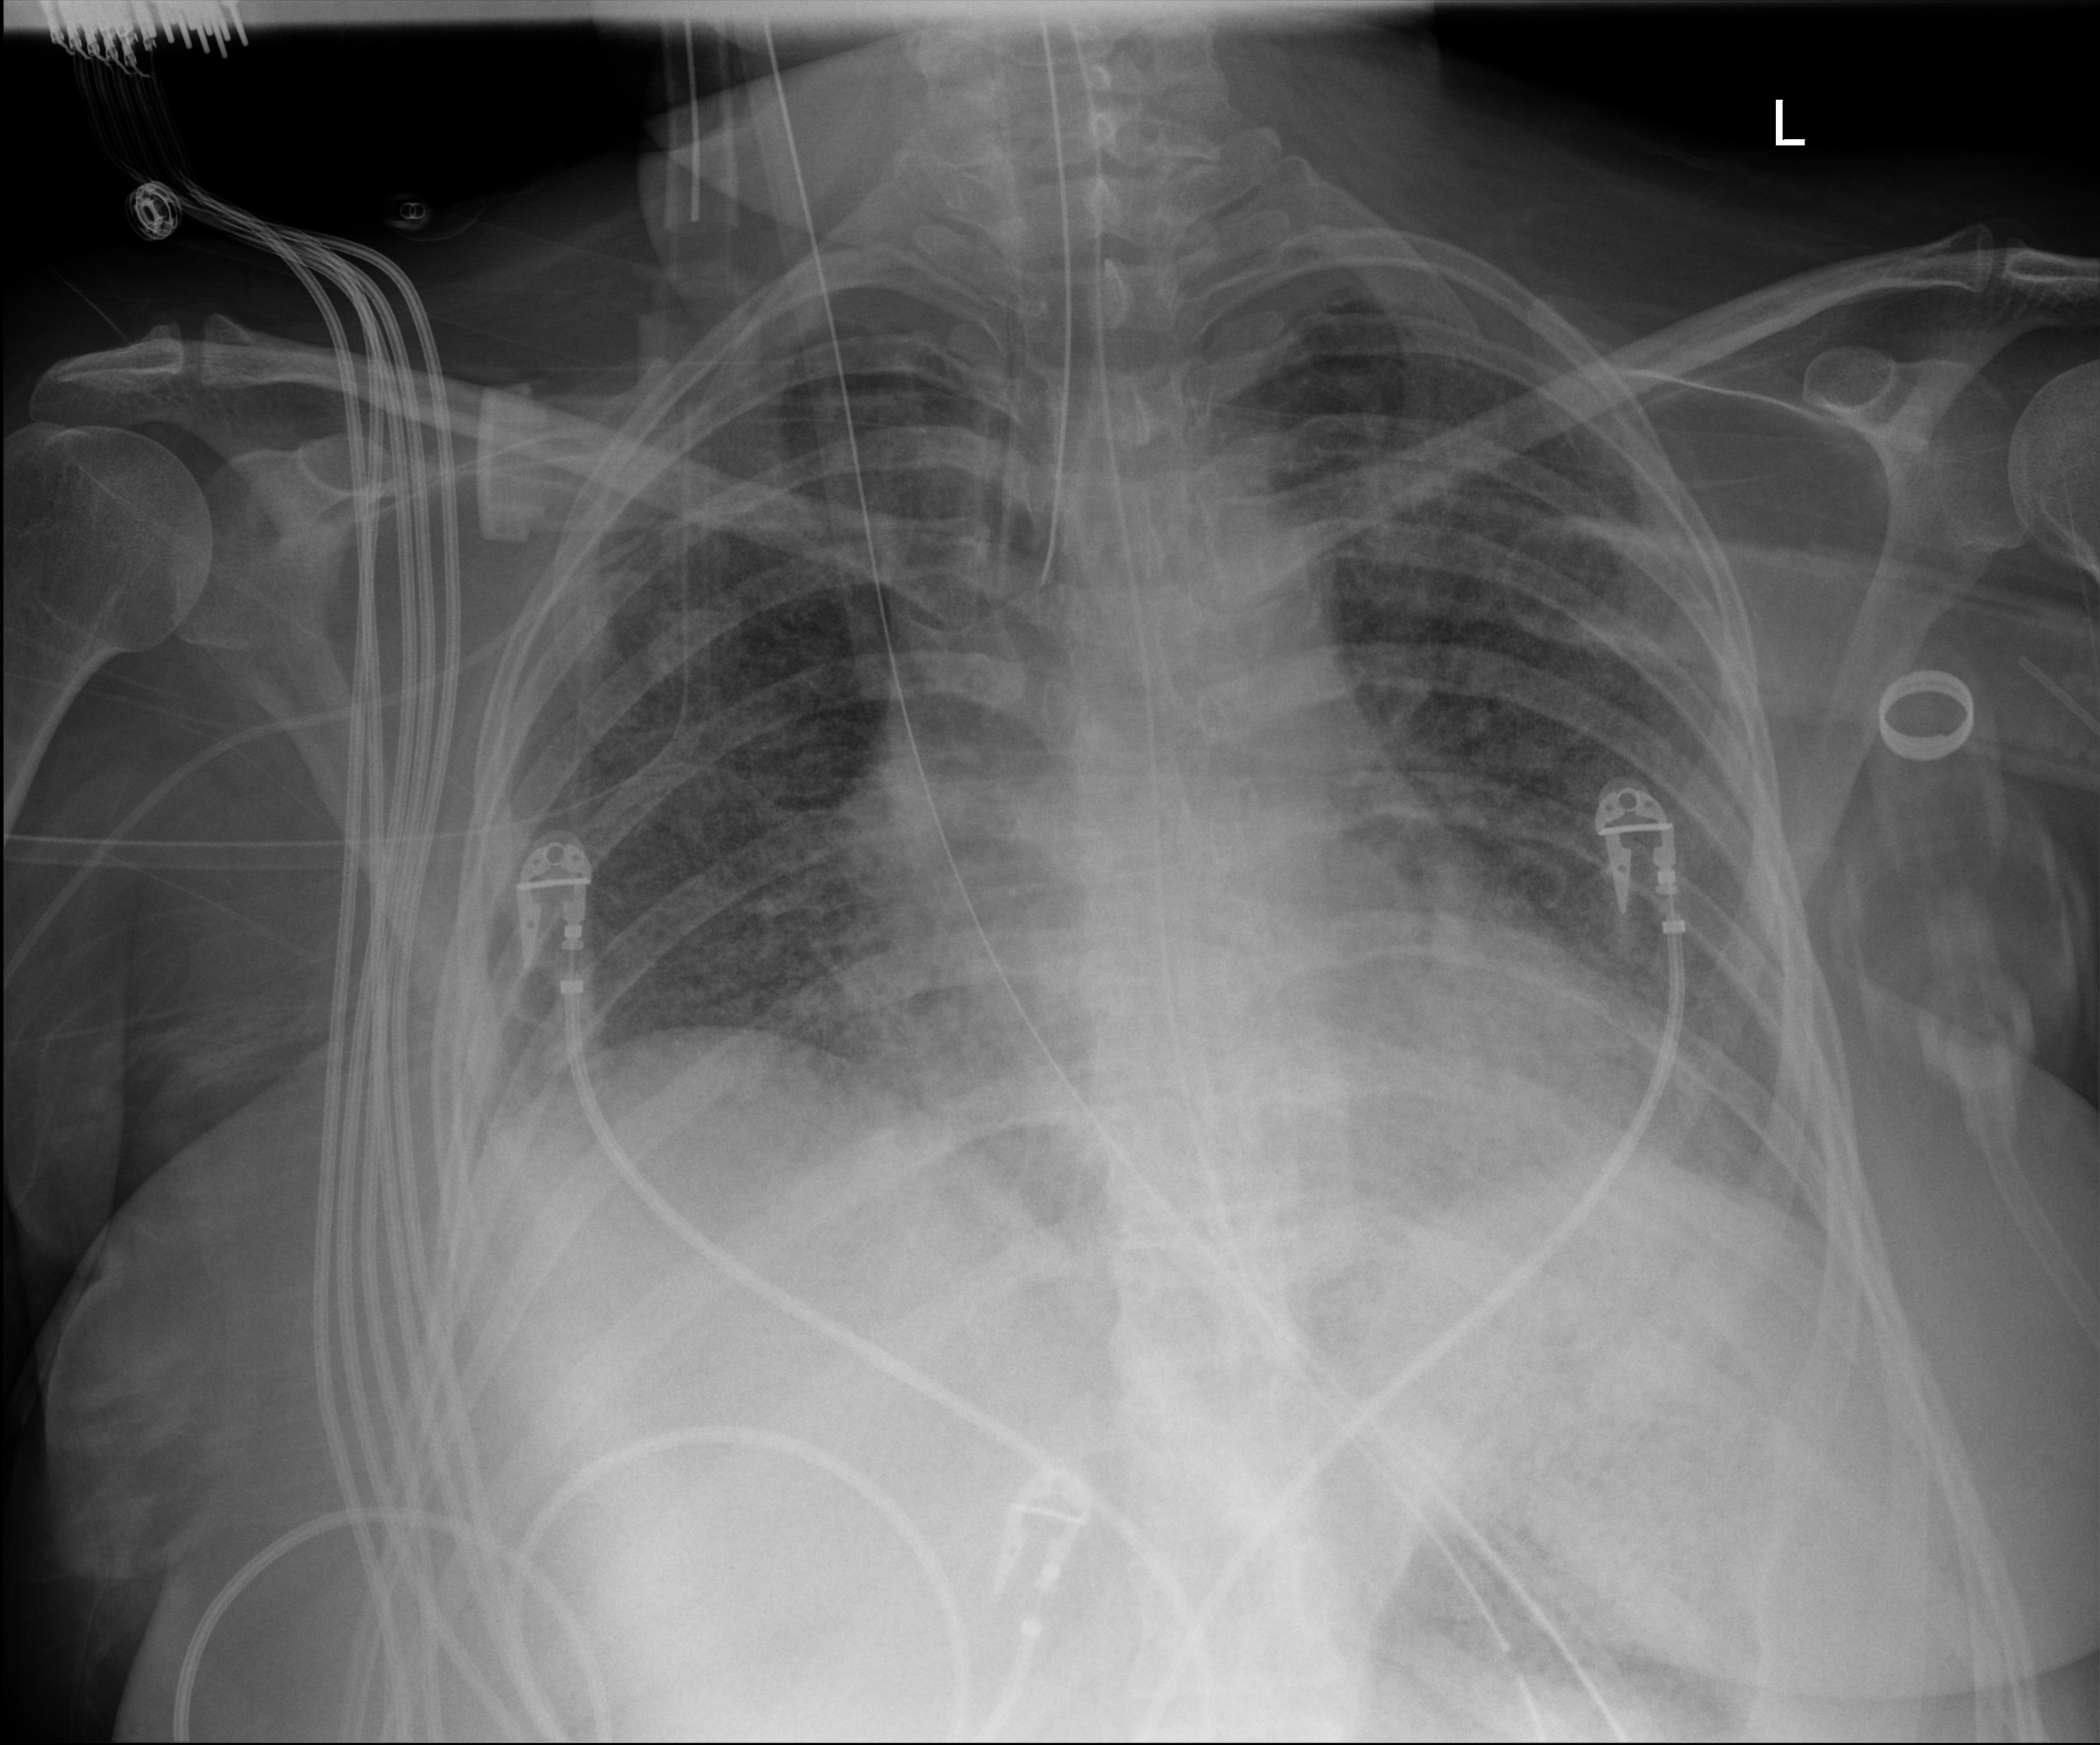
Bedside chest radiograph (digital radiography). Patient hospitalised with COVID-19; female, aged 18–59 years.
Admission-level facts for this patient (not findings on this image; timing relative to this image not recorded): mechanically ventilated during this hospital stay: yes; admitted to intensive care during this hospital stay: yes.